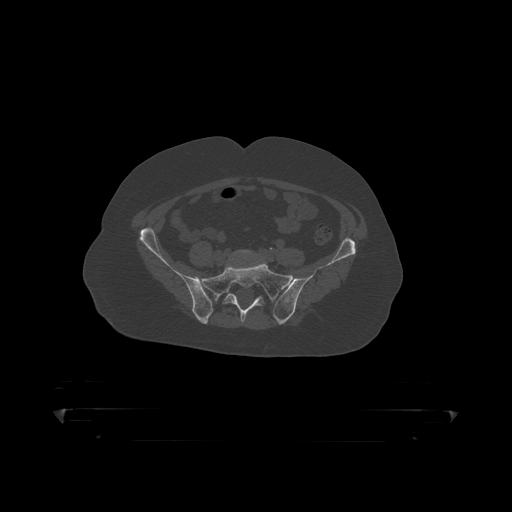
CT including the spine, one axial slice; position 19 of 390 along the scan axis; 120 kVp; bone window (W 1800 / L 400 HU); 1.25 mm slice thickness; 512 × 512 image matrix, field of view 650 × 650 mm. Male patient, age 60 years. From the clinical record (not read from this slice): primary cancer: prostate.
Structures marked on this image (semi-automatically segmented with operator editing):
- L5 vertebra: bounding box <228,250,262,261> (left, top, right, bottom; pixels)